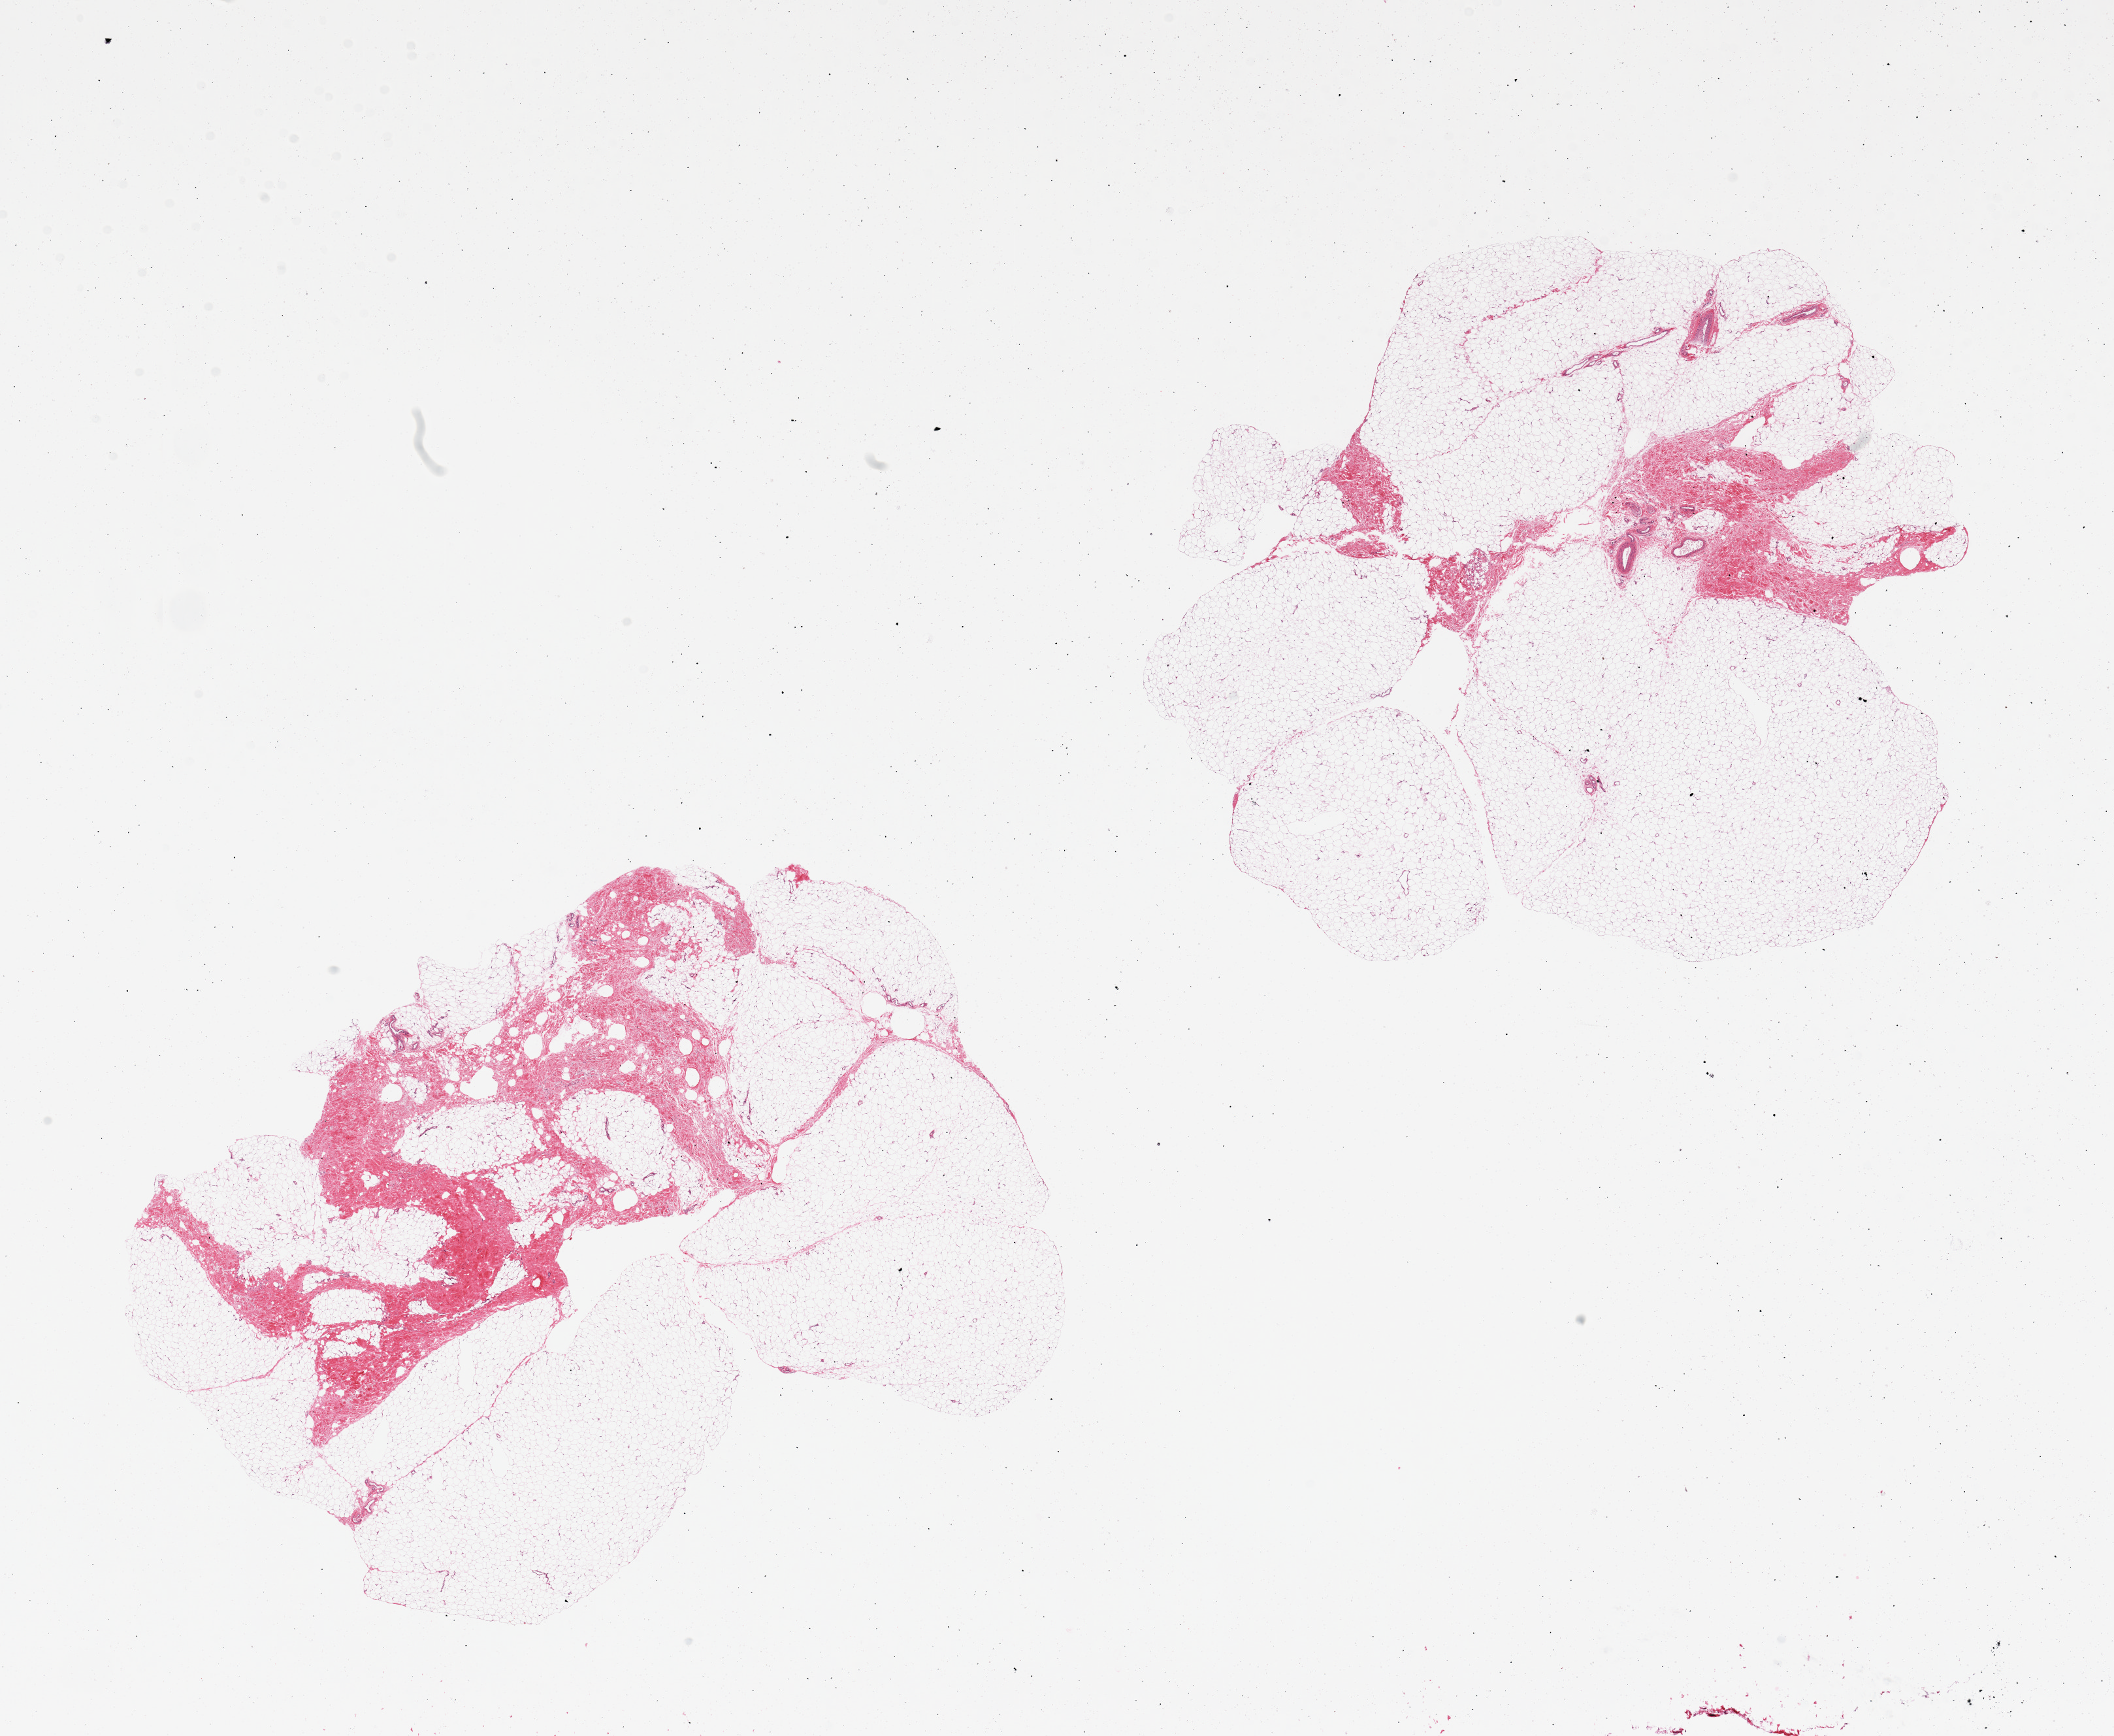
Digitized H&E-stained section — whole scanned area (about 25.6 x 21.0 mm) shown as a low-resolution overview. PAXgene-fixed, paraffin-embedded tissue. Sampled site (target tissue): adipose tissue. Donor tissue sample. Donor: male.
* reviewer comment on this tissue sample: 2 pieces; 20 and 30% fibrous component